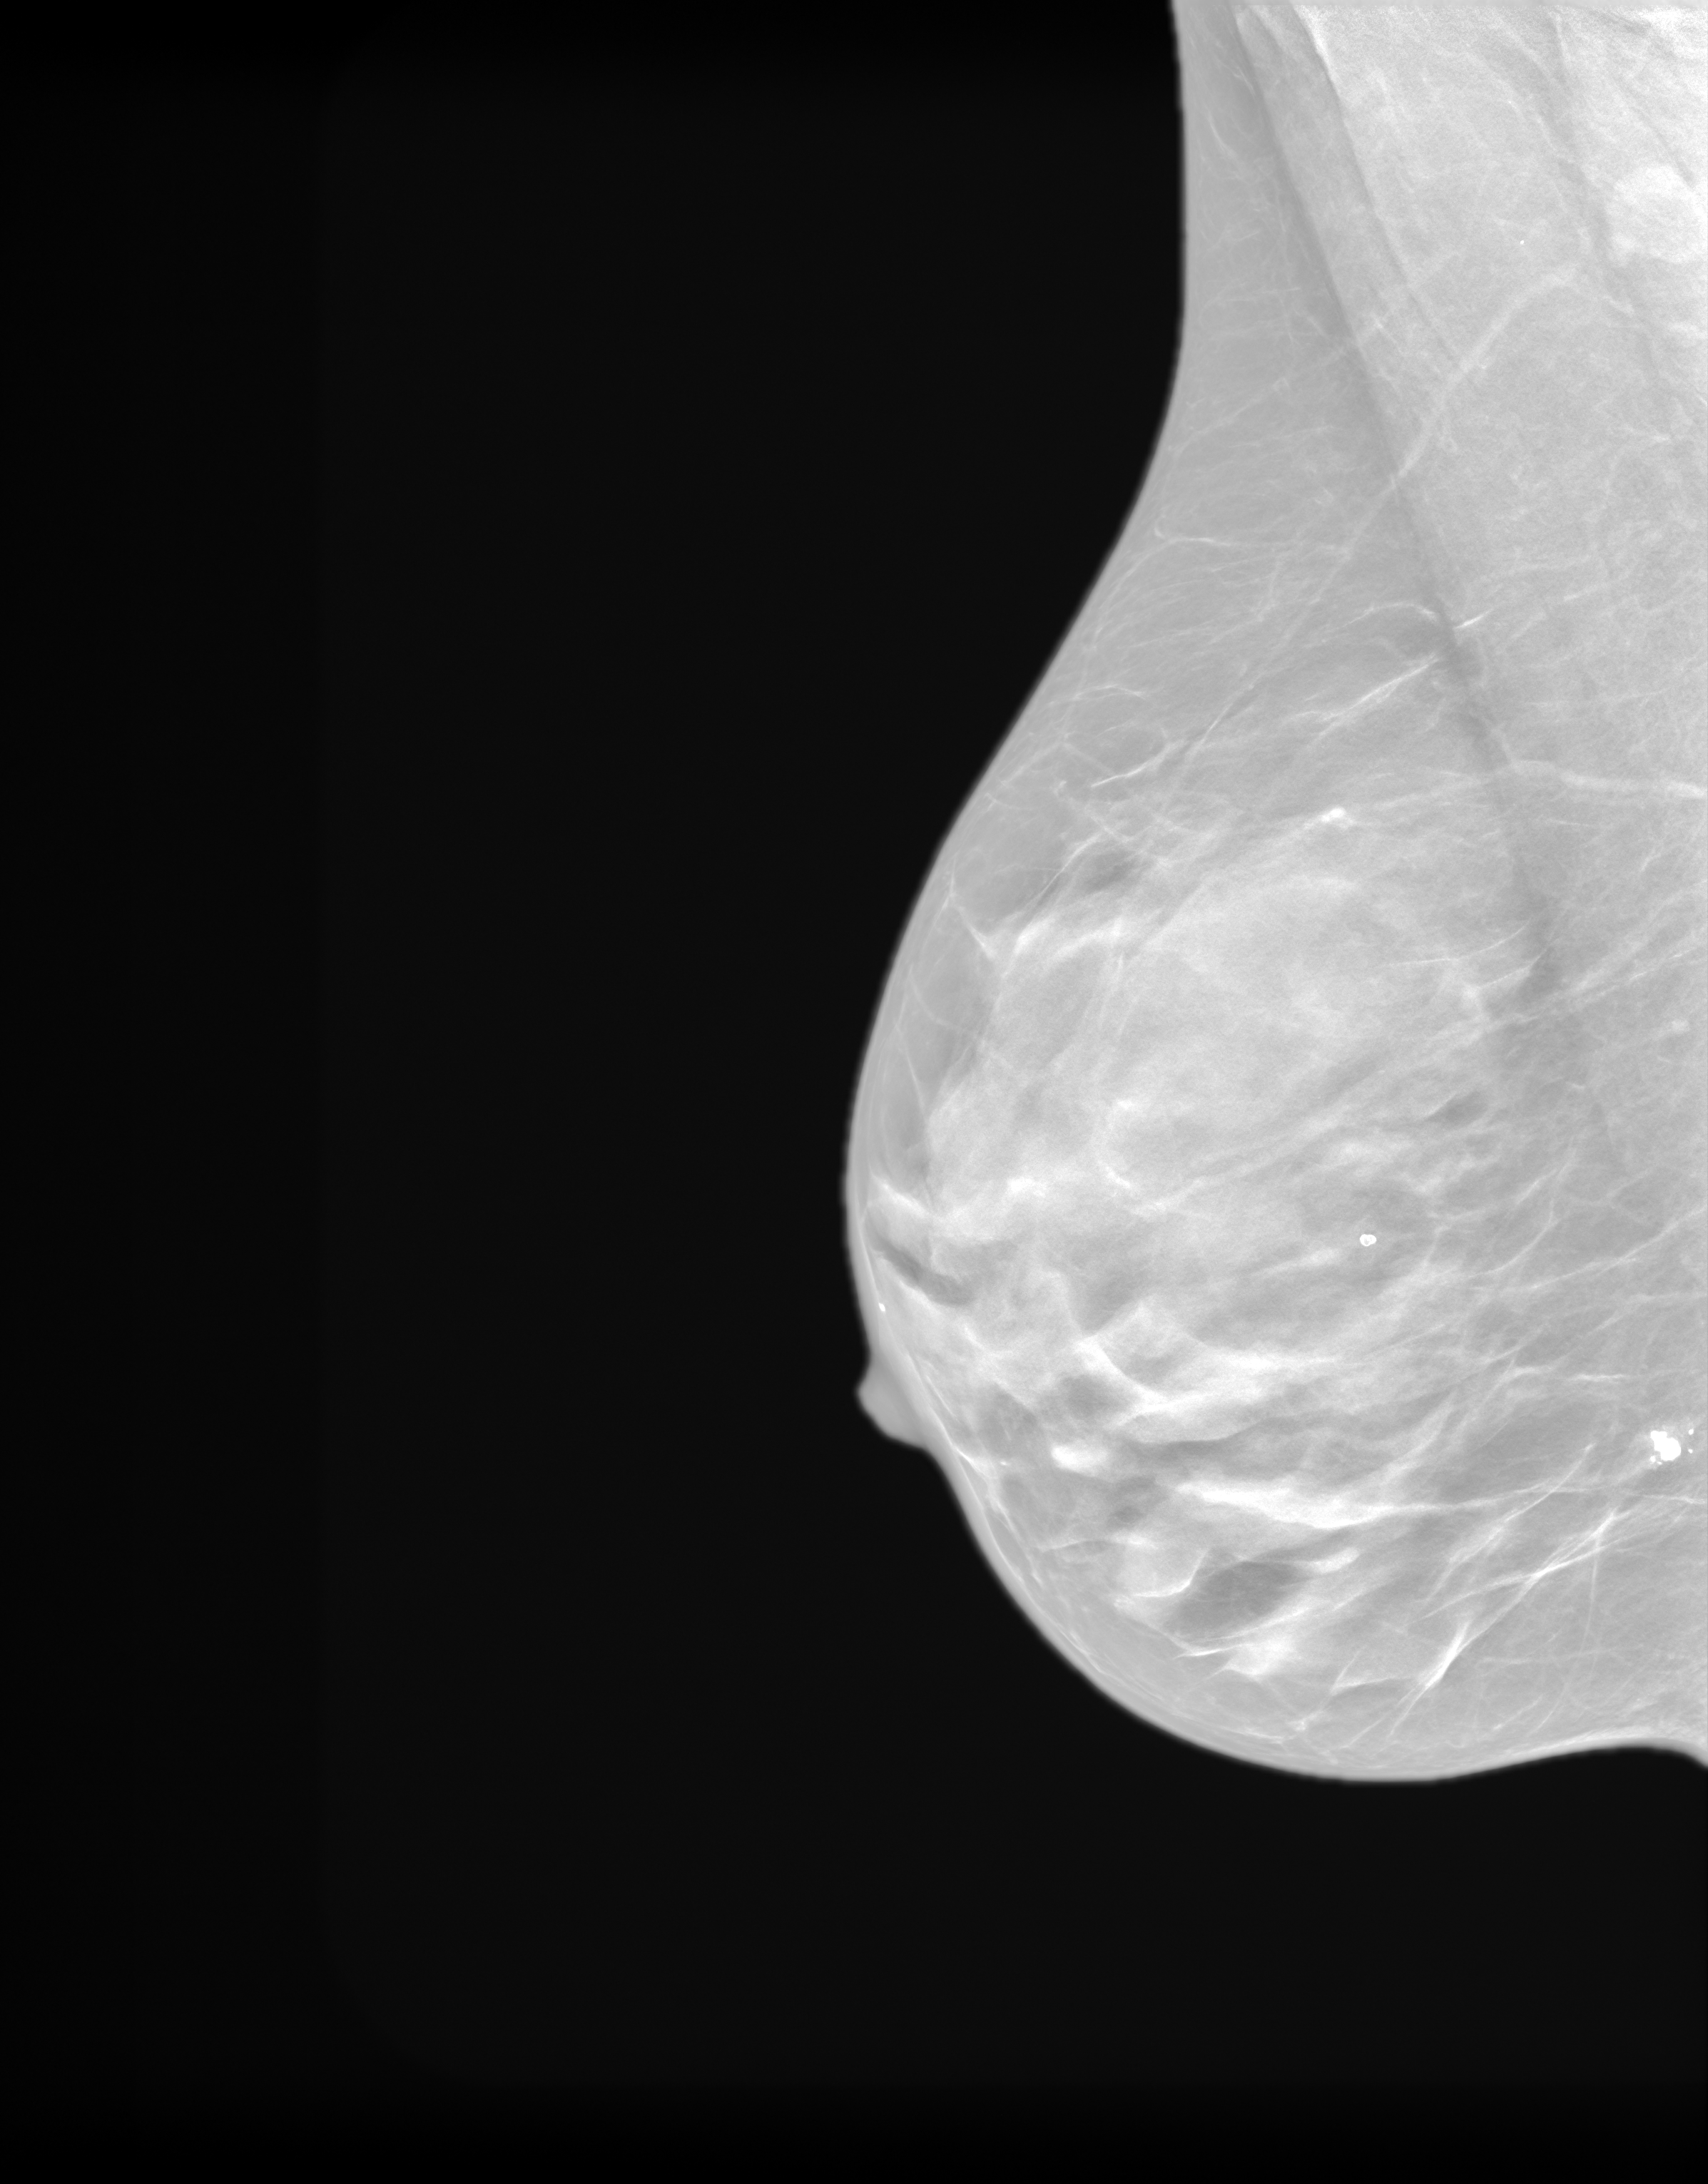
Screening examination; system: SenoIris_1SP1.1(421). Patient: female, 60 years.
Image type: synthesized 2-D view from tomosynthesis. Breast: right. Projection: mediolateral oblique (MLO) view. BI-RADS breast density category at the screening exam (both breasts, scale 1–4): 4. Final BI-RADS category for the screening round (tomosynthesis exam, both breasts): category 1. Recall: no recall after this screen.